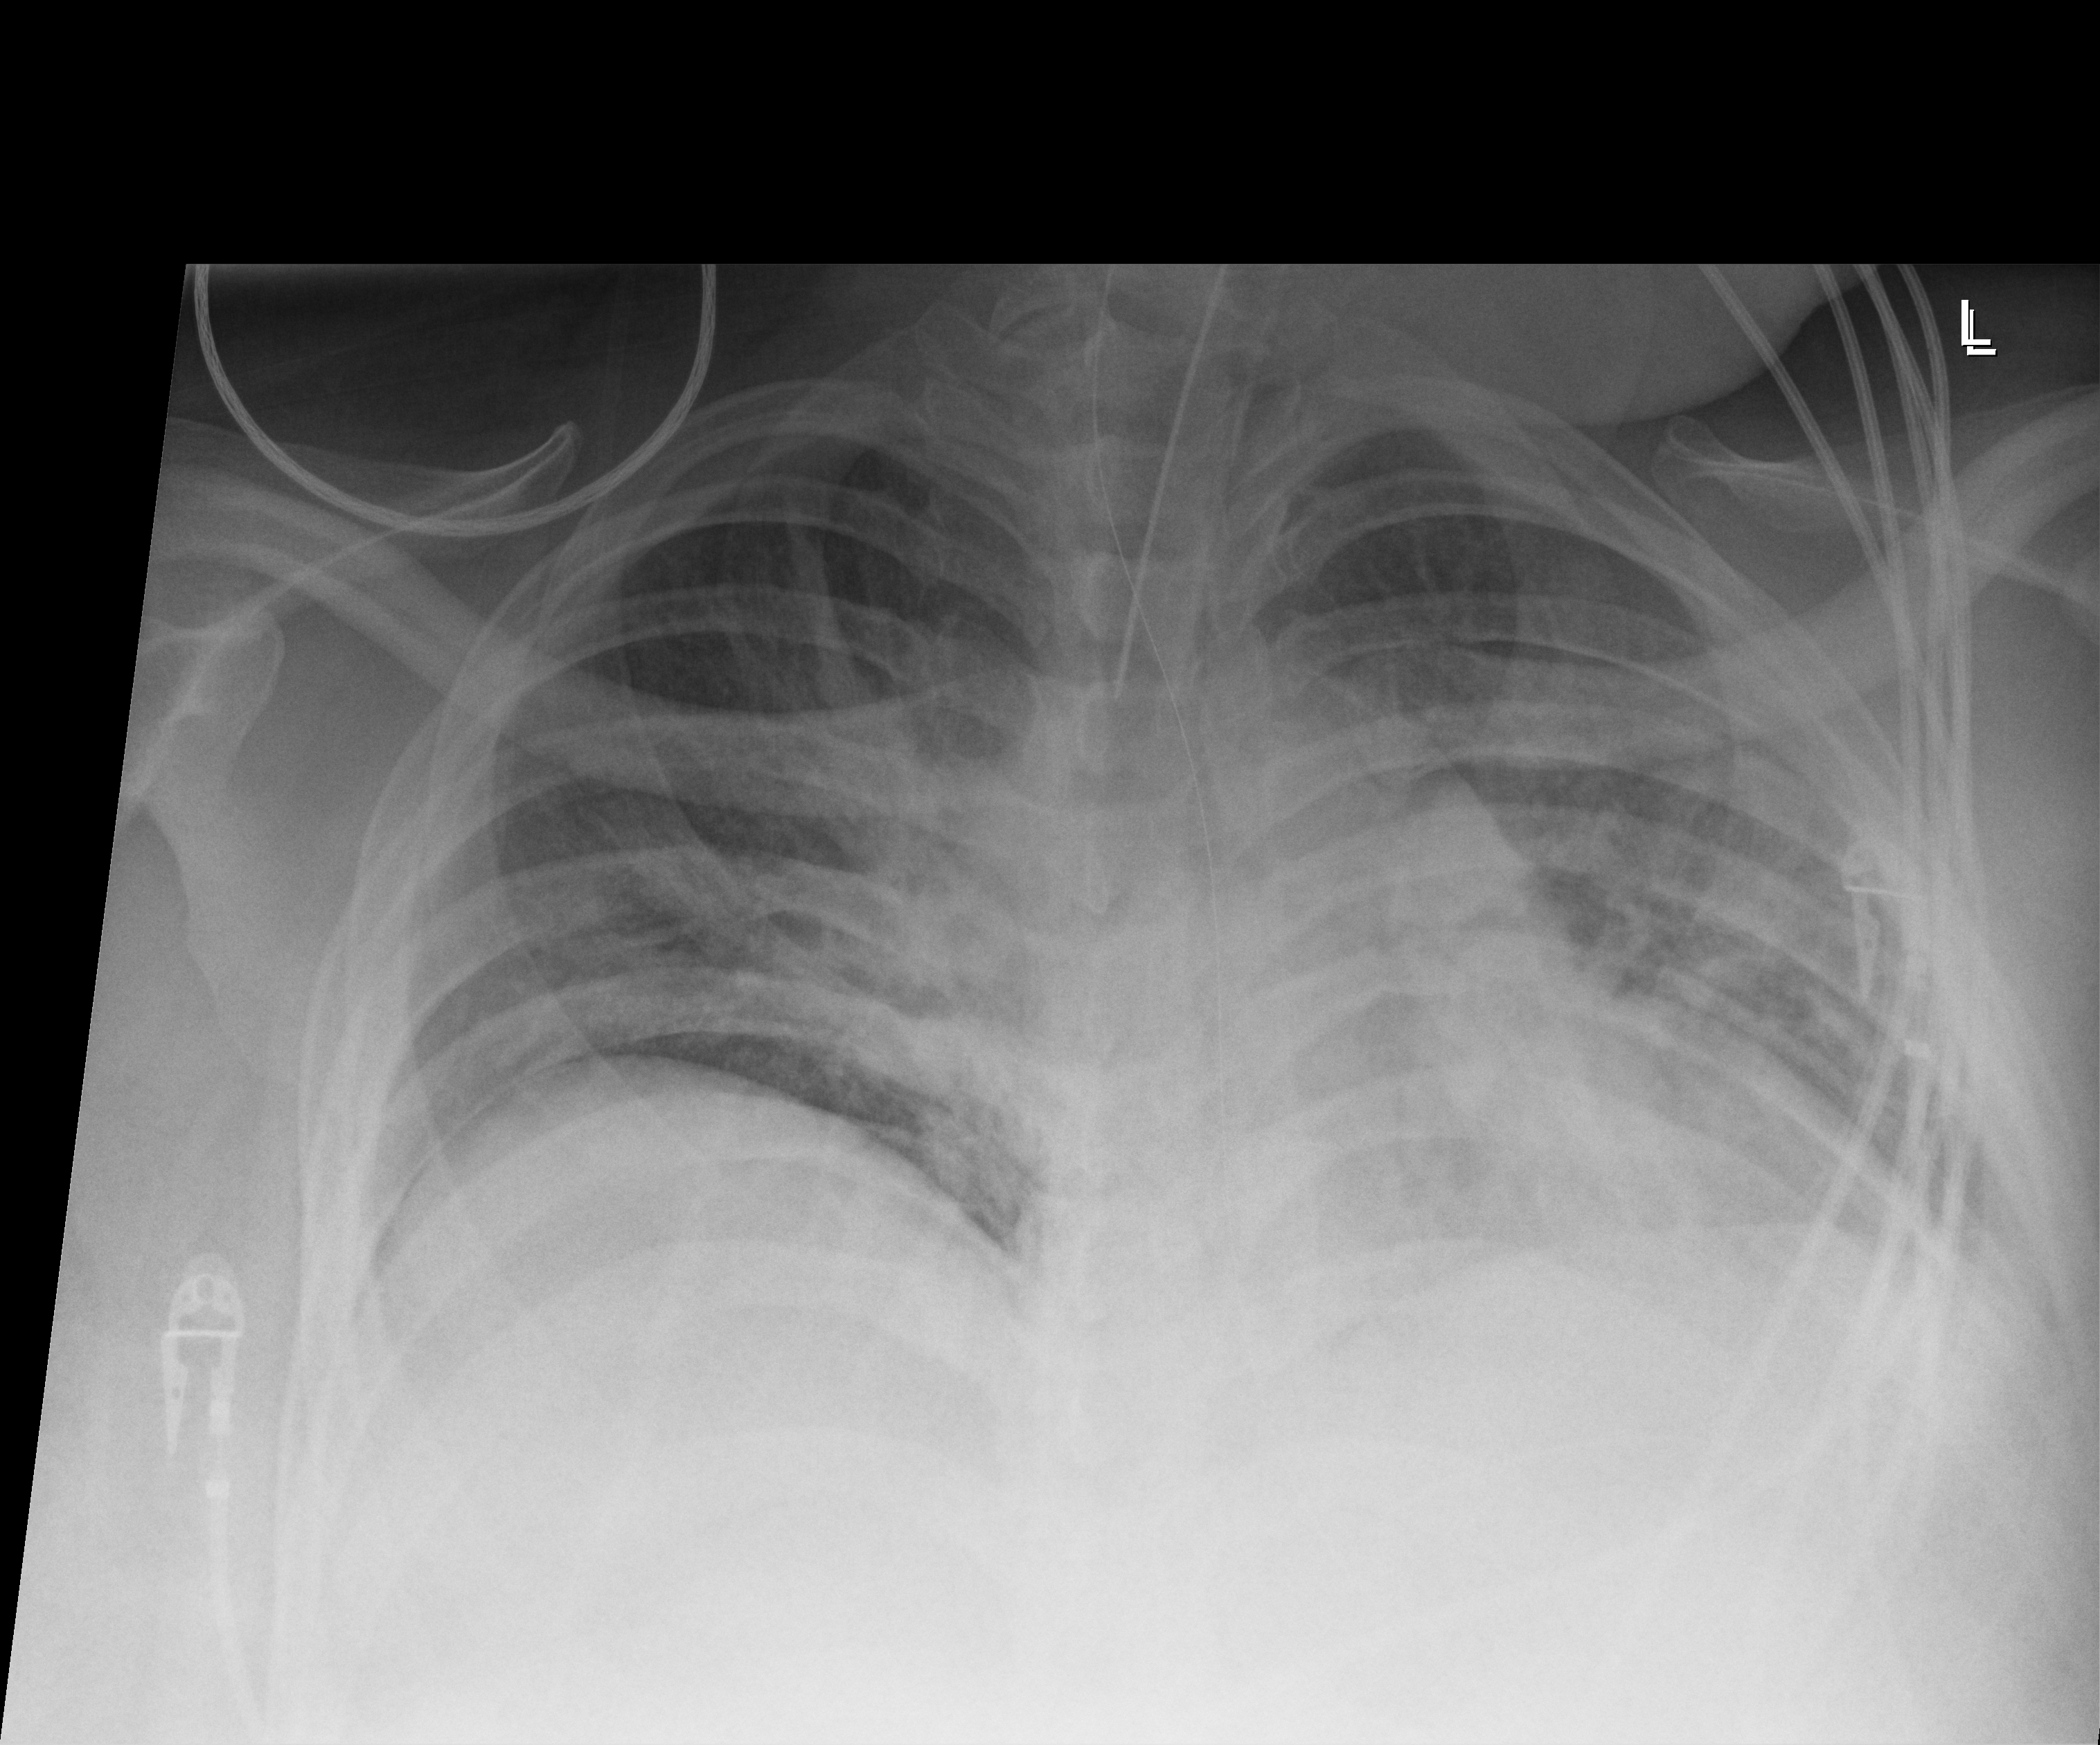
Bedside chest radiograph (digital radiography). Patient hospitalised with COVID-19; male, aged 18–59 years.
Admission-level facts for this patient (not findings on this image; timing relative to this image not recorded): admitted to intensive care during this hospital stay: yes; mechanically ventilated during this hospital stay: yes.